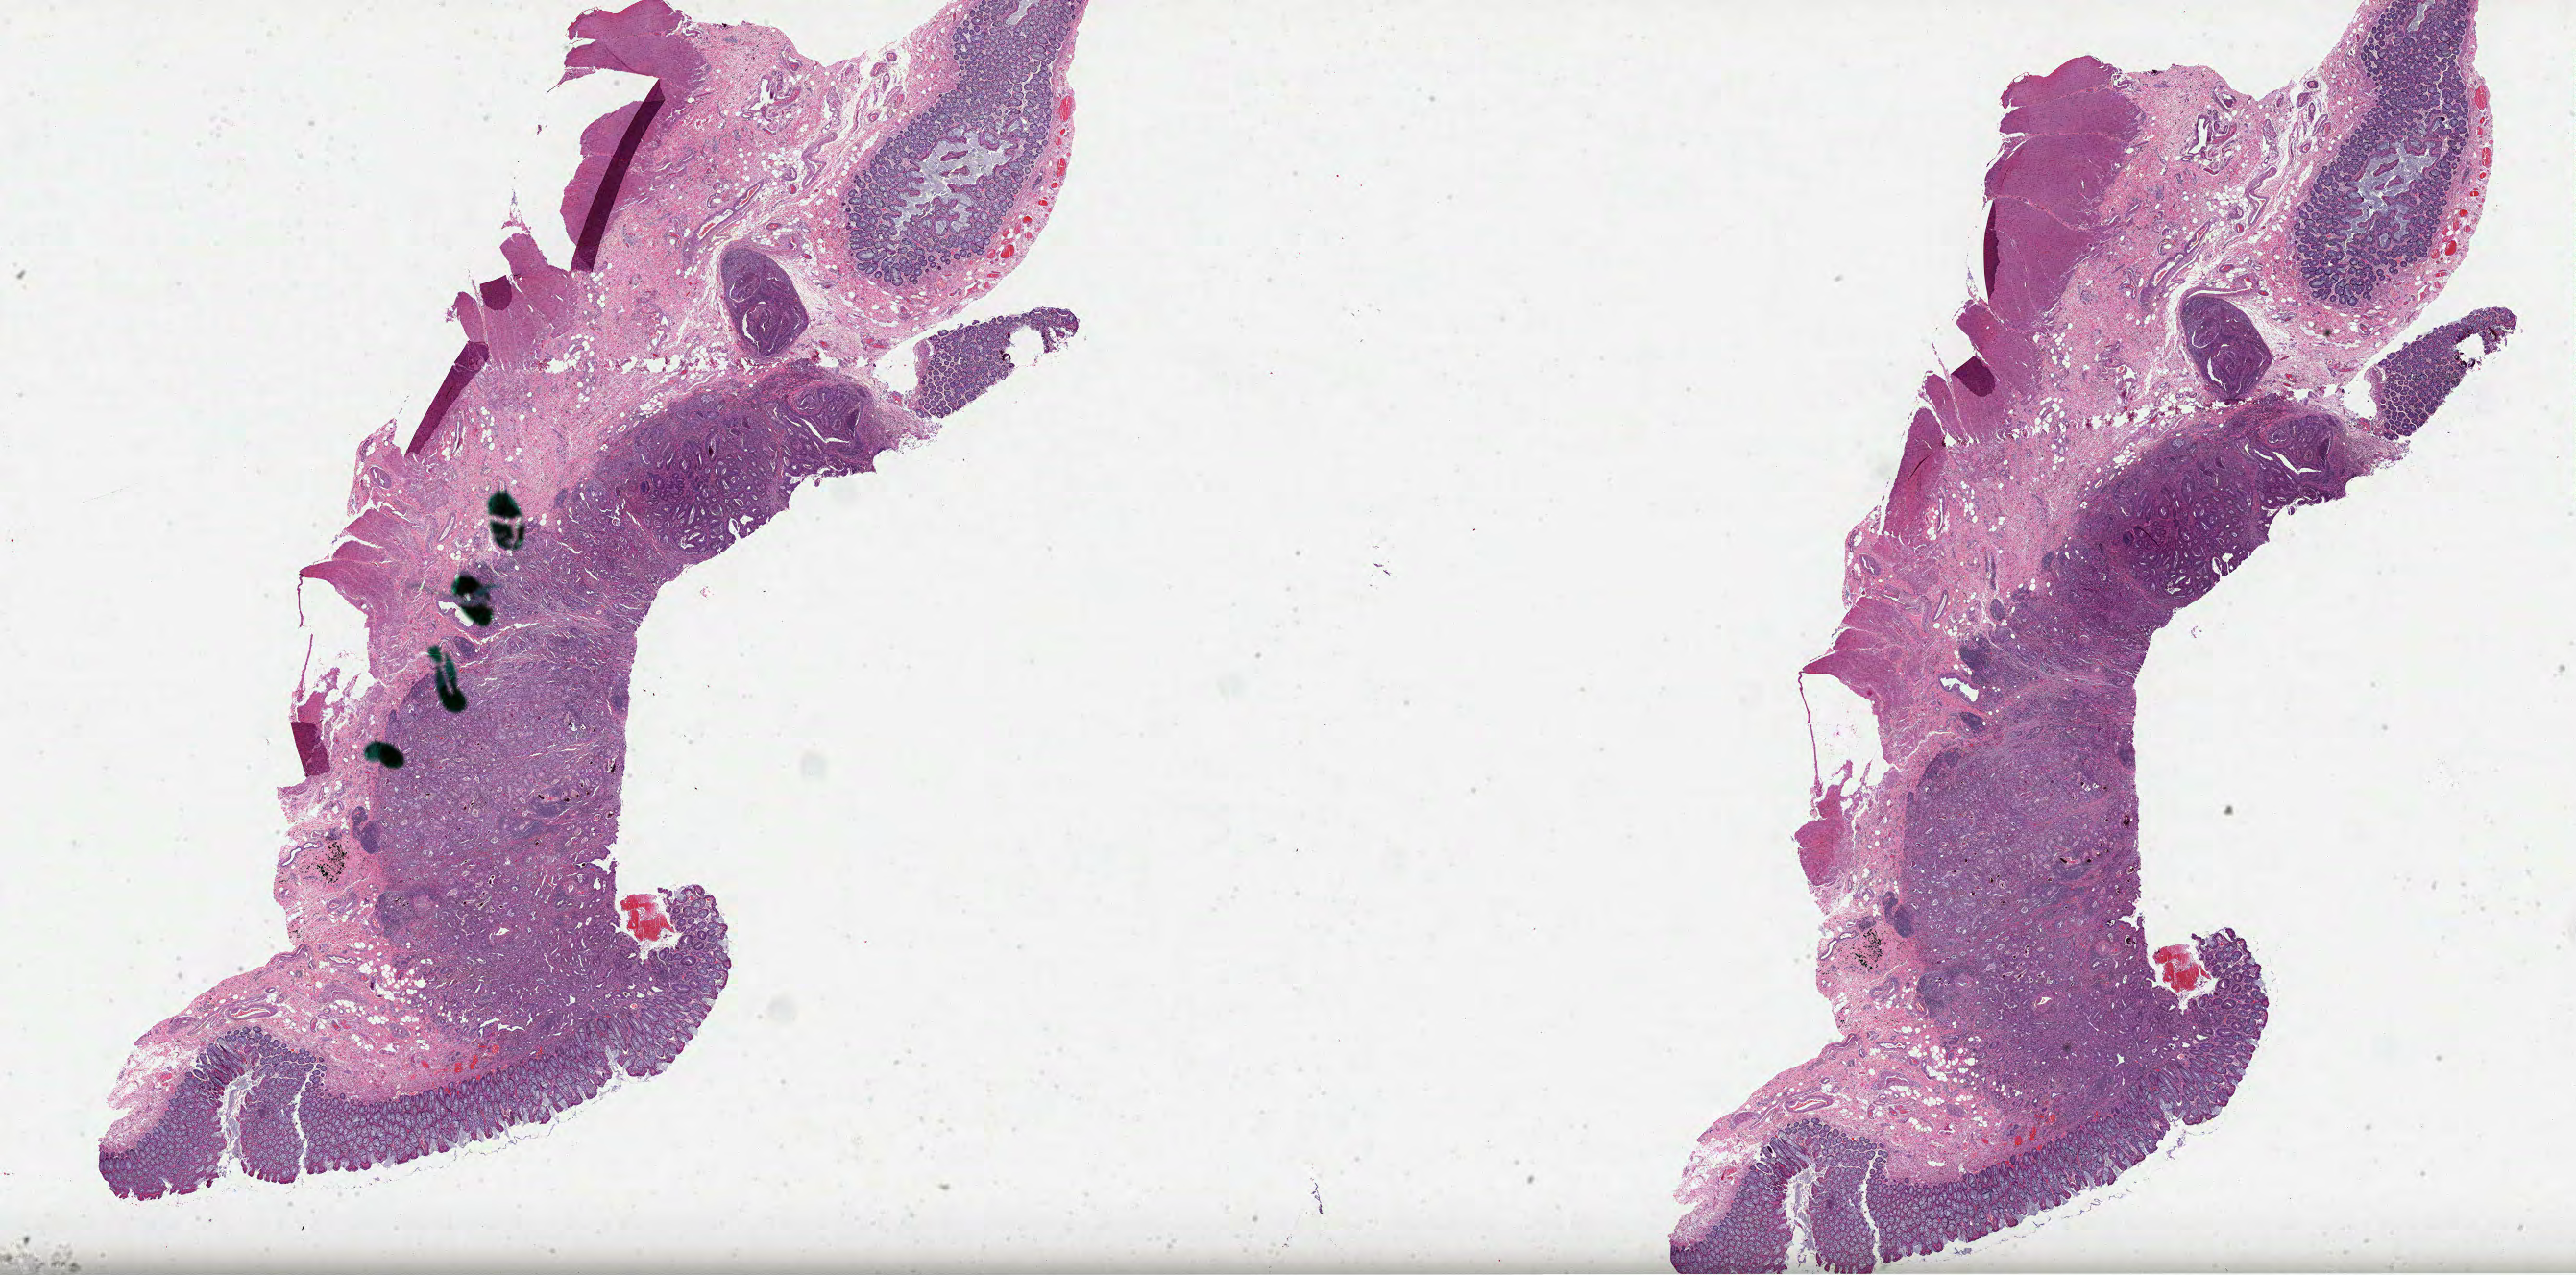
Whole-slide histology image, Hematoxylin and eosin (H&E) stained, shown as a low-resolution overview of the whole scanned area (about 43.3 x 21.4 mm, from a 40x scan), formalin-fixed paraffin-embedded (FFPE) diagnostic section, sample: primary tumour, colon. Male patient; age at initial diagnosis 74 years.
Diagnosis: Adenocarcinoma, NOS.